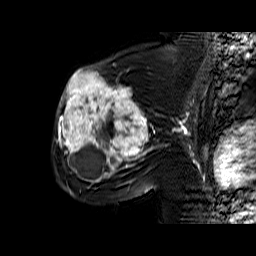
Breast MRI (dynamic contrast-enhanced), one sagittal slice; slice 37 of 60 in the series (ordered by position); dynamic contrast-enhanced series, time point 2 of 6 at this slice position (early post-contrast); 1.5 T; TE 6.4 ms, TR 32.9 ms; 256 × 256 image matrix. Female patient. From the clinical record (not read from this slice): setting: breast cancer imaged before/during neoadjuvant chemotherapy; receptor status: triple-negative.
Outlined on this slice (semi-automatically segmented with operator editing):
- analysis volume of interest (the breast-tissue region the enhancement analysis was run in; not a lesion): bounding box <55,65,157,174> (left, top, right, bottom; pixels)
- tumour enhancement mask (voxels above the 100 % enhancement threshold inside the analysis volume of interest): <58,70,154,174>